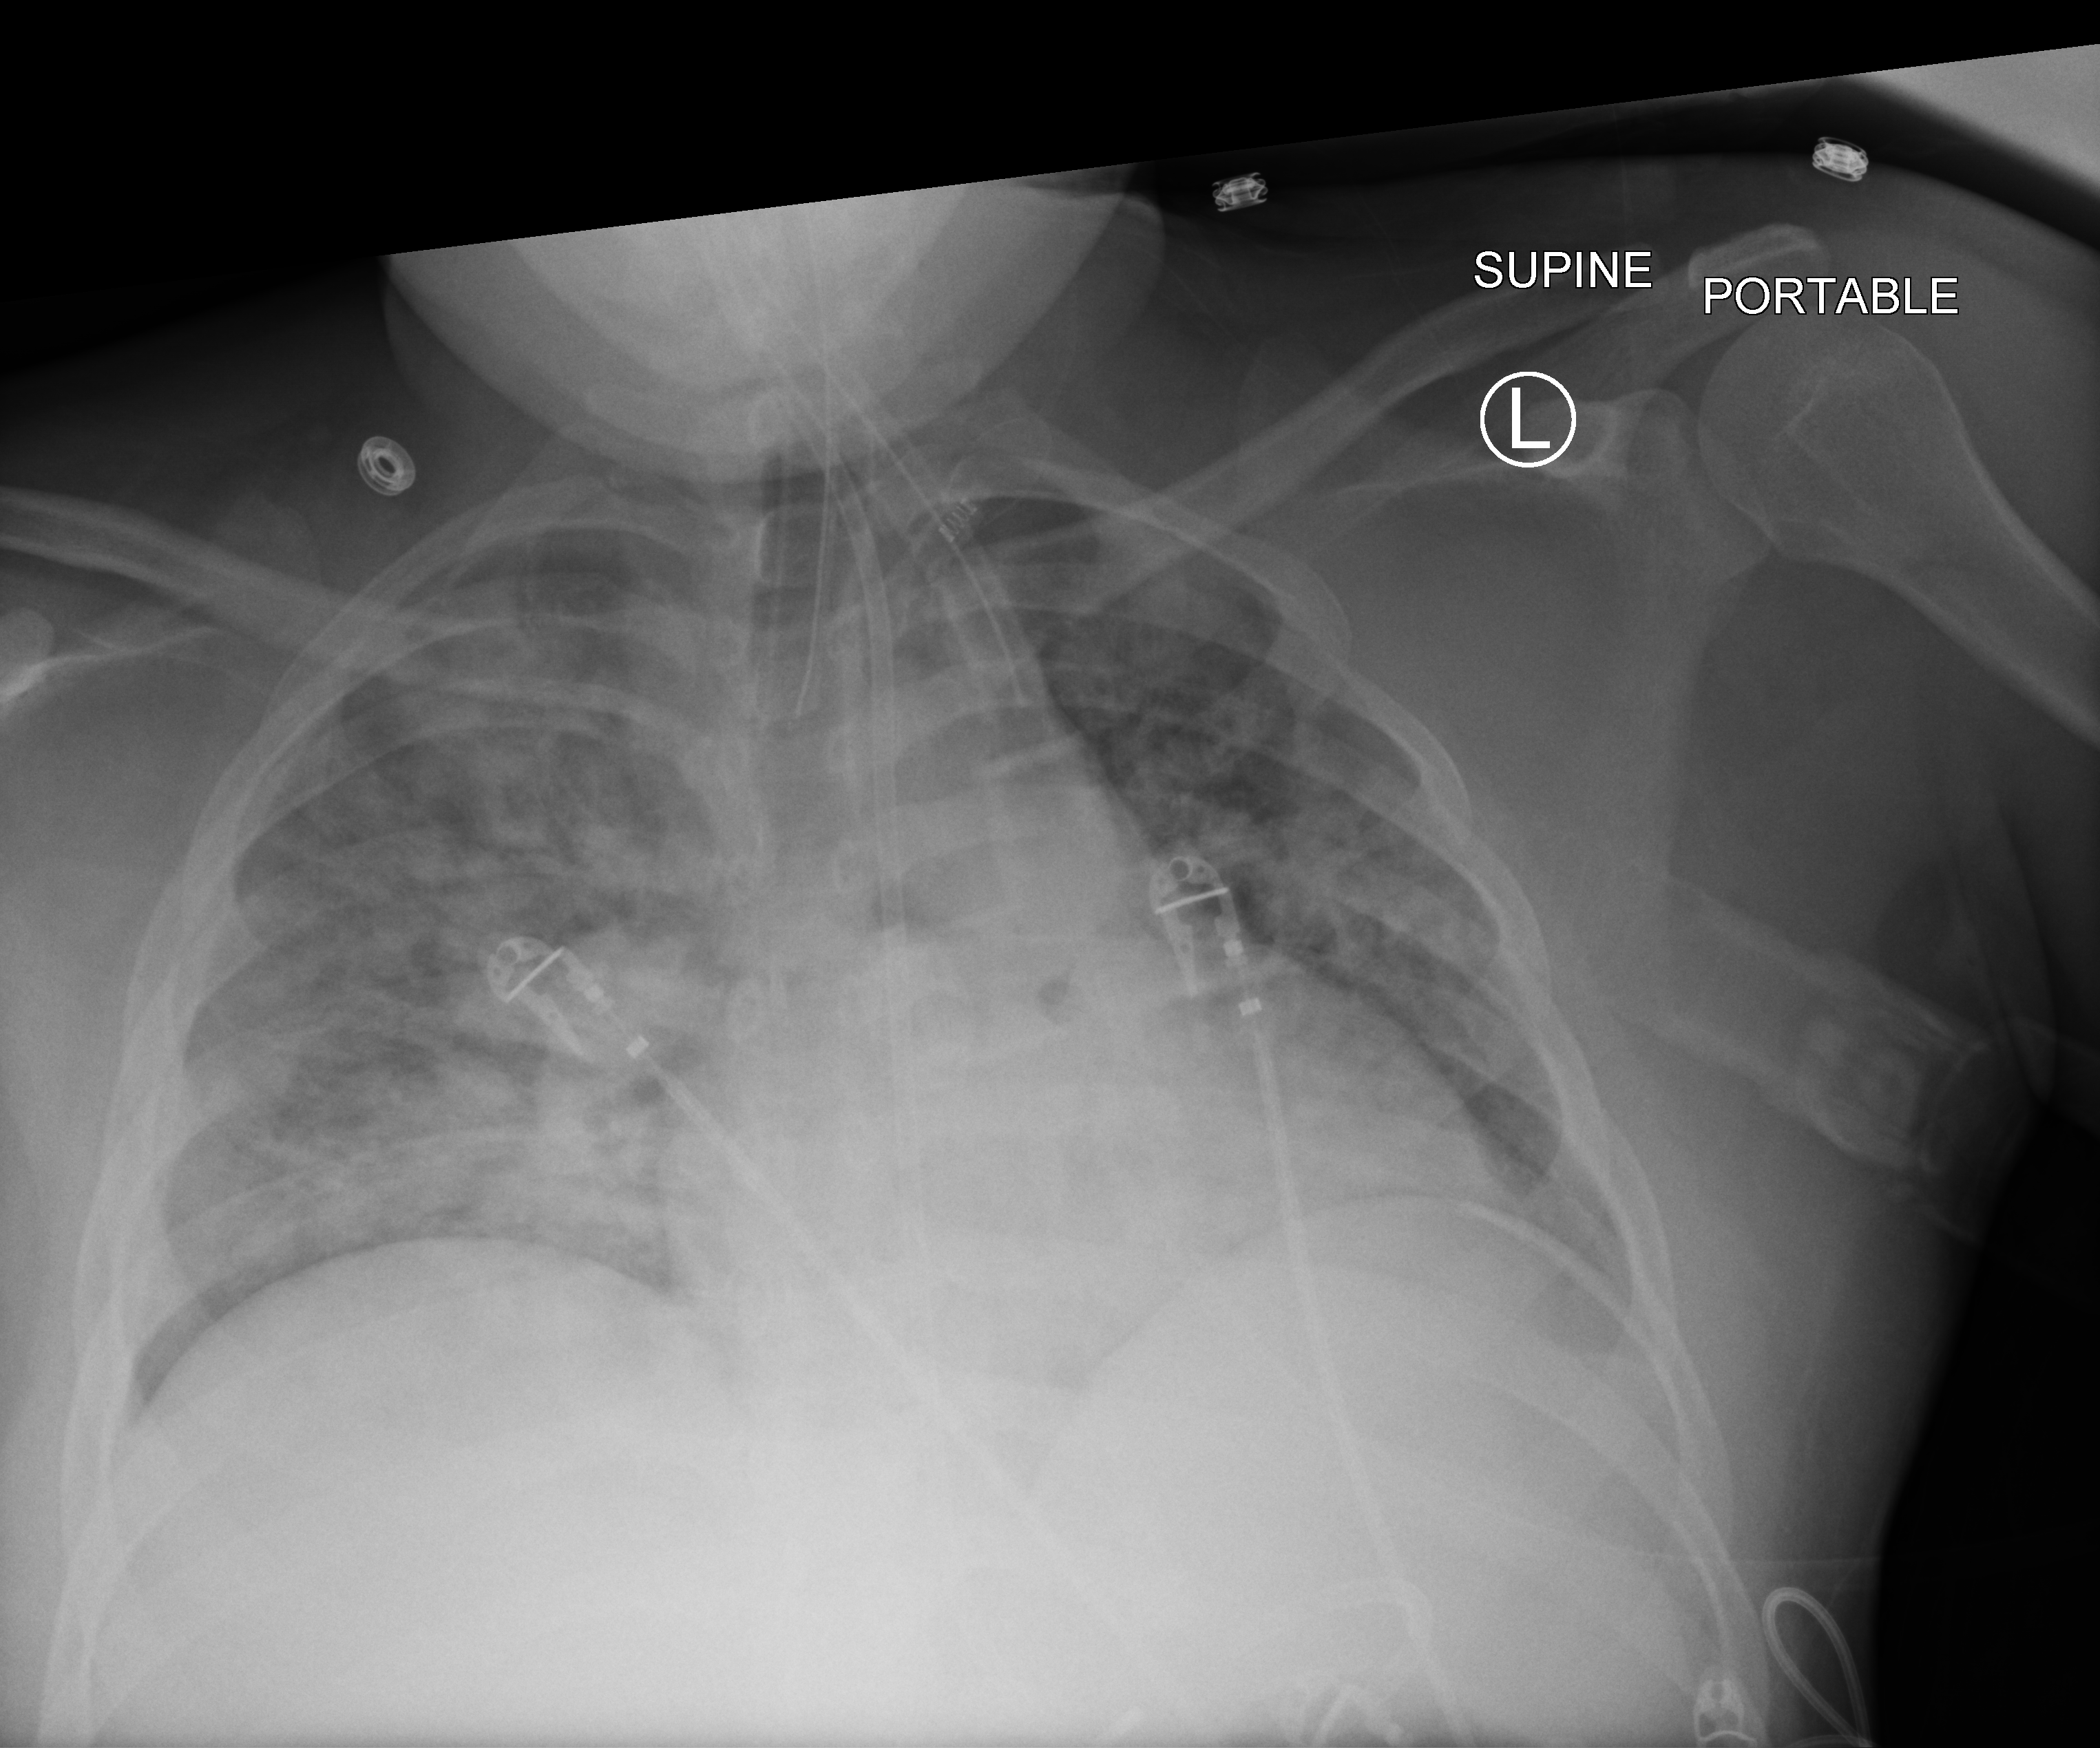
Portable chest radiograph. Patient hospitalised with COVID-19; male, aged 18–59 years.
From the hospital-stay record, not from the radiograph (when in the stay this image was taken is not recorded): COPD (admission record): no.